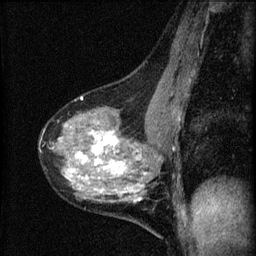
Breast MRI (dynamic contrast-enhanced), one sagittal slice; position 33 of 60 along the scan axis; dynamic contrast-enhanced series, image 2 of 4 at this slice position (ordered by acquisition); 1.5 T; TE 4.2 ms, TR 8.2 ms; 2 mm slice thickness; 256 × 256 image matrix, field of view 180 × 180 mm. Patient: female, 41 years.
Outlined on this slice (semi-automatically segmented with operator editing):
- analysis volume of interest (the breast-tissue region the enhancement analysis was run in; not a lesion): bounding box <40,91,166,203> (left, top, right, bottom; pixels)
- tumour enhancement mask (voxels above the 70 % enhancement threshold inside the analysis volume of interest): <52,130,147,201>